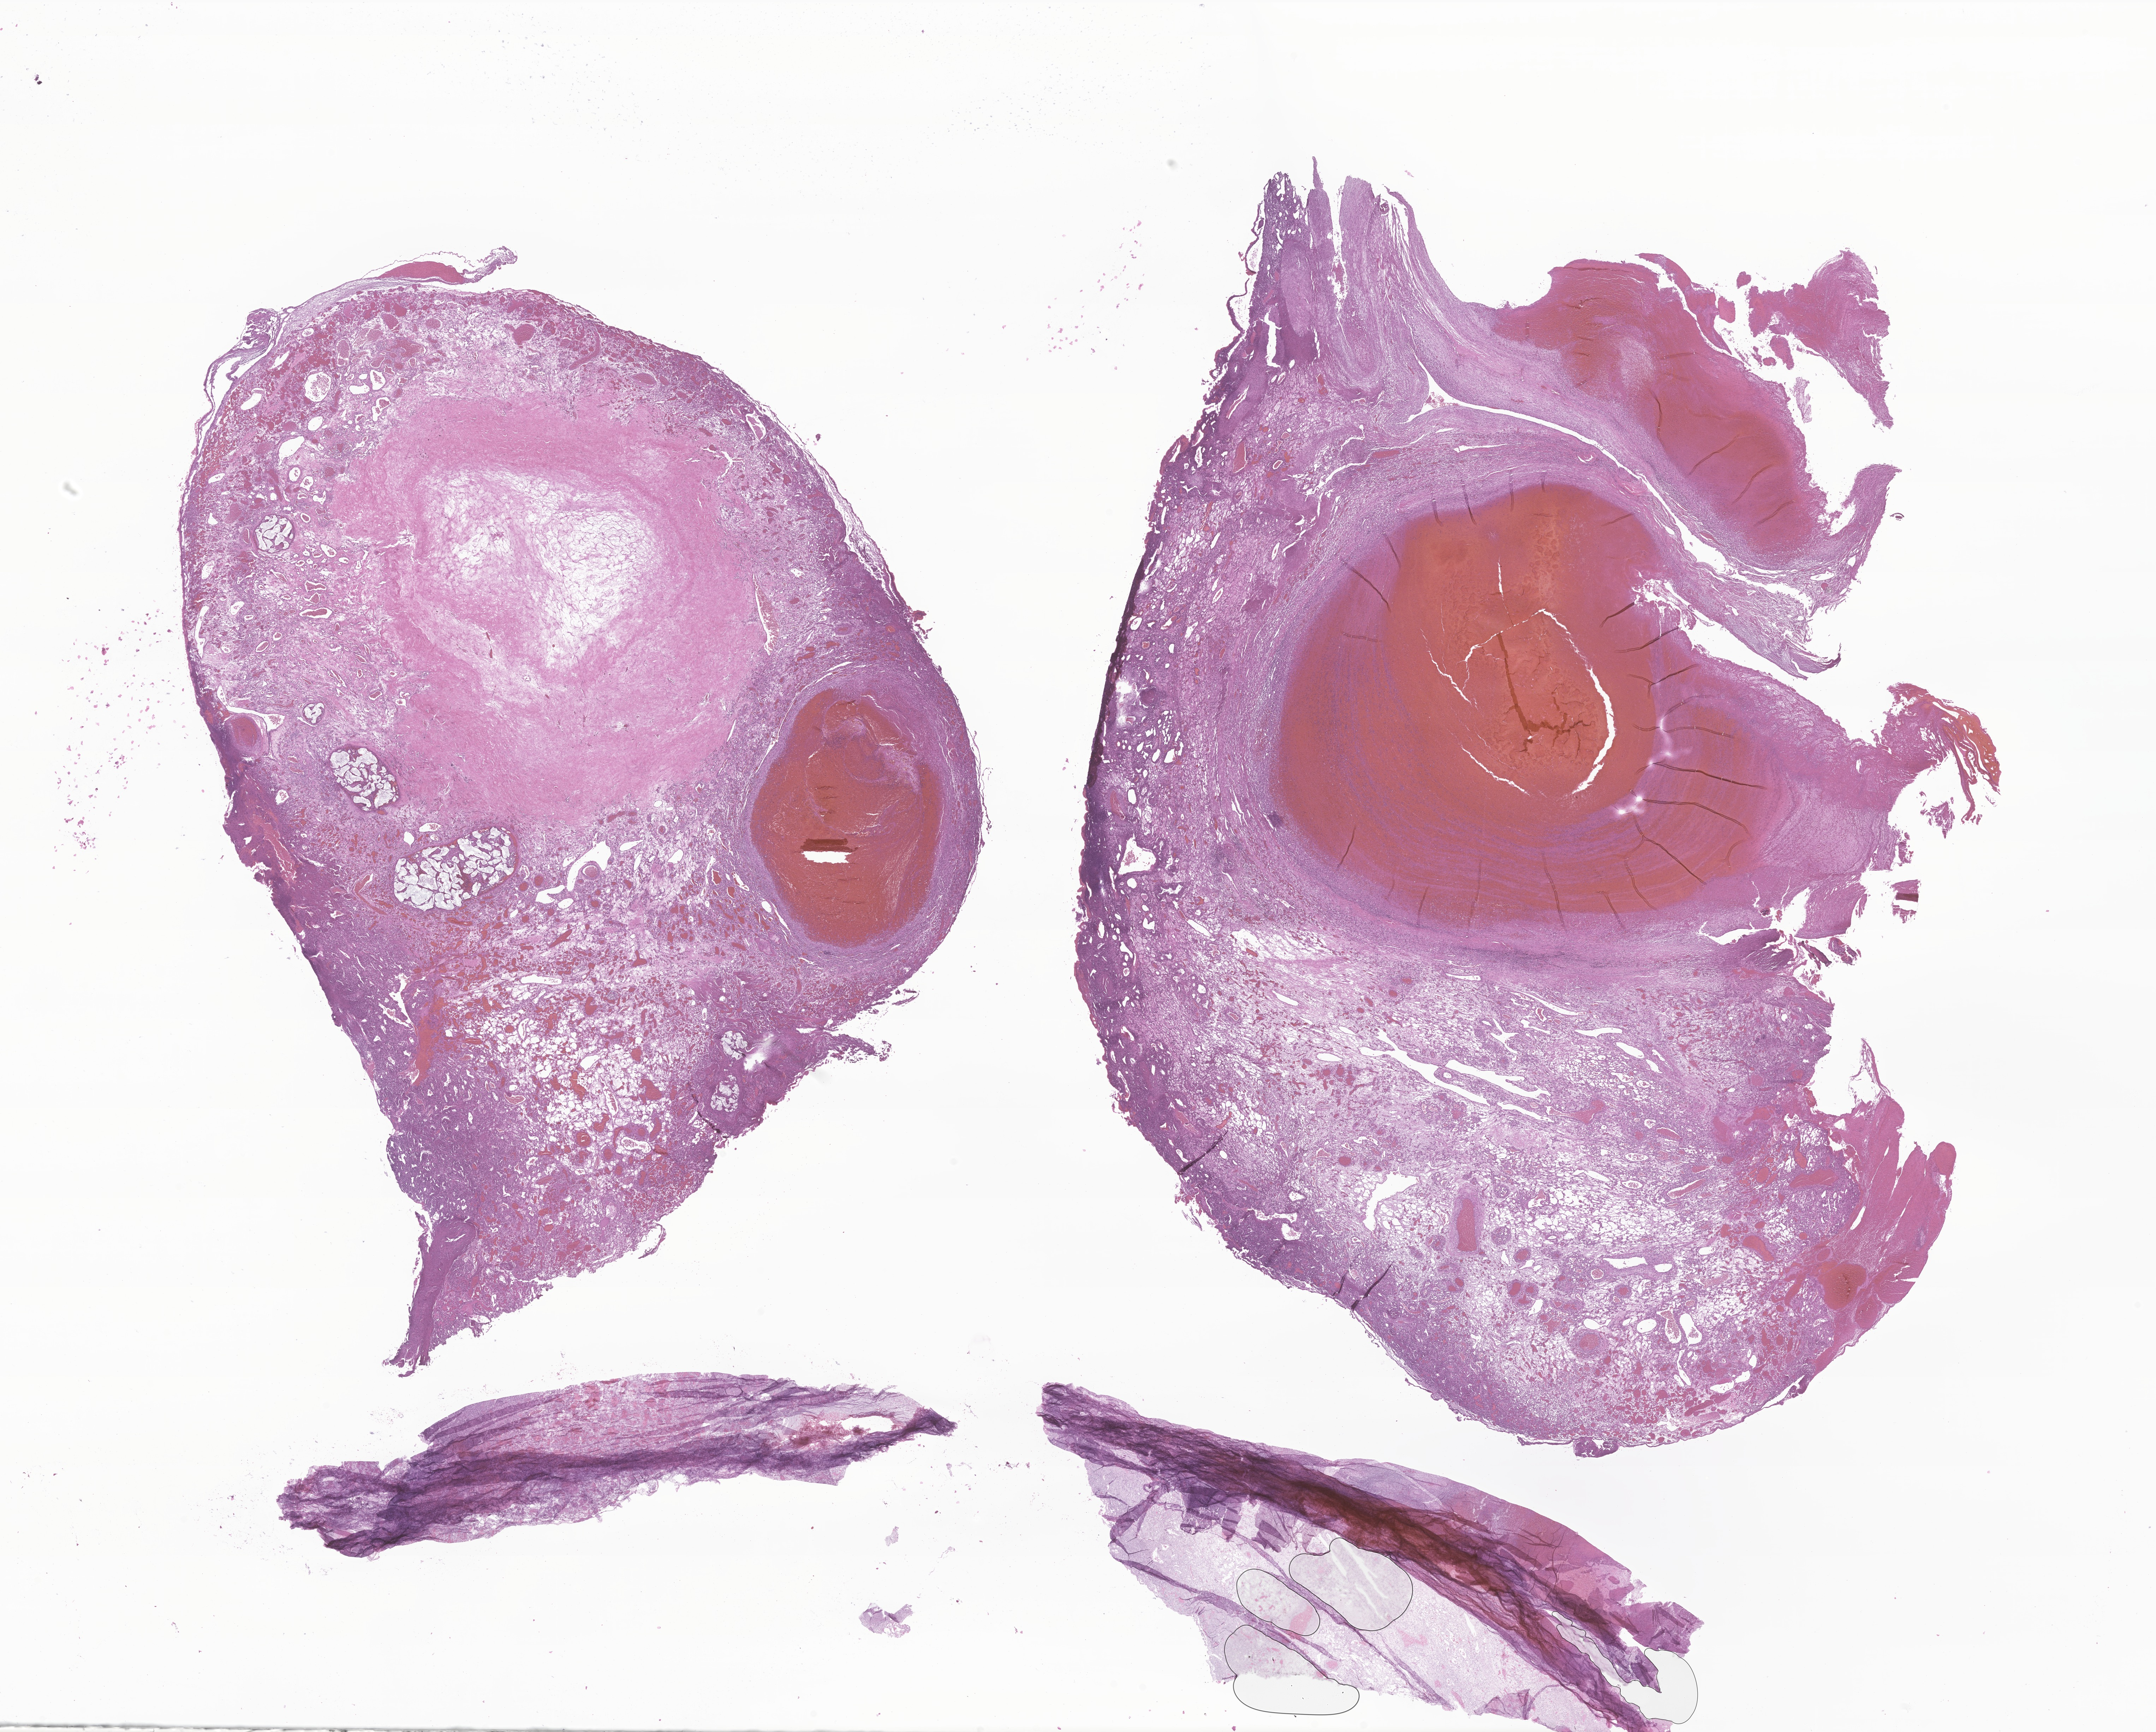
Whole-slide image, H&E stain of tumor tissue from the brain, whole scanned area (about 25.7 x 20.7 mm) shown as a low-resolution overview; formalin-fixed paraffin-embedded section. Patient female; age 93 months (7 years 9 months).
• diagnosis: Malignant tumor, spindle cell type